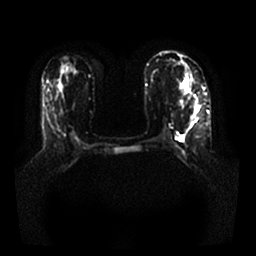
Breast MRI, one axial slice; slice 14 of 25 in the series (ordered by position); diffusion-weighted series; image 2 of 4 stored at this slice position (different b-values; order by instance number); 1.5 T; 4 mm slice thickness; 256 × 256 image matrix. Female patient.
Annotated regions visible in this slice (outlined manually by an expert reader):
- tumour on diffusion-weighted imaging: box from (x=194, y=108) to (x=199, y=113) px